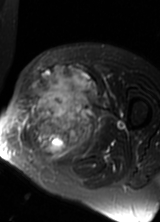
MRI of an extremity soft-tissue mass, one axial slice; position 39 of 69 along the scan axis; T2-weighted fat-saturated; MR volume resampled by the dataset authors to the PET/CT grid (not the native acquisition matrix); 3.27 mm slice thickness; 160 × 222 image matrix, field of view 156 × 217 mm. Female patient. From the clinical record (not read from this slice): histological type: pleomorphic leiomyosarcoma; grade: high; site of the primary tumour: left thigh.
Annotated regions visible in this slice (expert contour drawn on MRI and transferred to this co-registered scan by the dataset authors):
- gross tumour volume including surrounding oedema: bounding box (x1, y1, x2, y2) in pixels: (22, 66, 99, 162)
- gross tumour volume (mass): (25, 66, 97, 153)